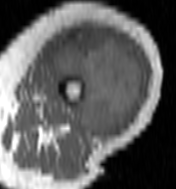
MRI of an extremity soft-tissue mass, one axial slice. Slice 49 of 100 in the series (ordered by position). MR volume resampled by the dataset authors to the PET/CT grid (not the native acquisition matrix). 176 × 189 image matrix, field of view 172 × 185 mm. Female patient. From the clinical record (not read from this slice): histological type: undifferentiated – high grade; grade: high; site of the primary tumour: left thigh.
Outlined on this slice (expert contour drawn on MRI and transferred to this co-registered scan by the dataset authors):
- gross tumour volume including surrounding oedema: bounding box (x1, y1, x2, y2) in pixels: (51, 30, 145, 138)
- gross tumour volume (mass): (53, 30, 143, 138)